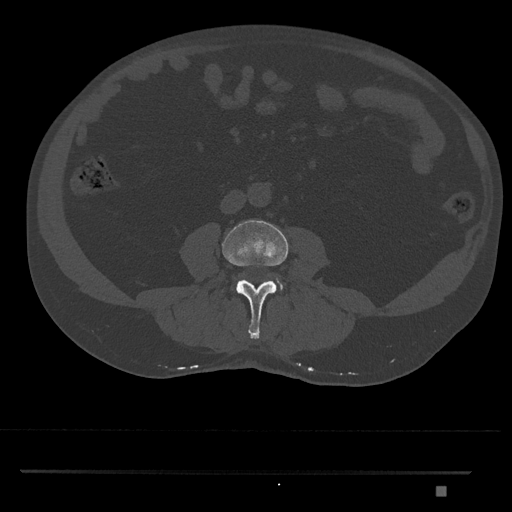
CT including the spine, one axial slice. Slice 665 of 1134 in the series (ordered by position). Reconstruction kernel Br40s/3. Bone window (W 1800 / L 400 HU). 0.5 mm slice thickness. 512 × 512 image matrix, field of view 429 × 429 mm. Male patient, age 65 years. From the clinical record (not read from this slice): primary cancer: prostate.
Structures marked on this image (semi-automatic segmentation, software-assisted and operator-edited):
- L3 vertebra: bounding box (x1, y1, x2, y2) in pixels: (222, 220, 289, 339)
- L4 vertebra: (276, 278, 283, 290)